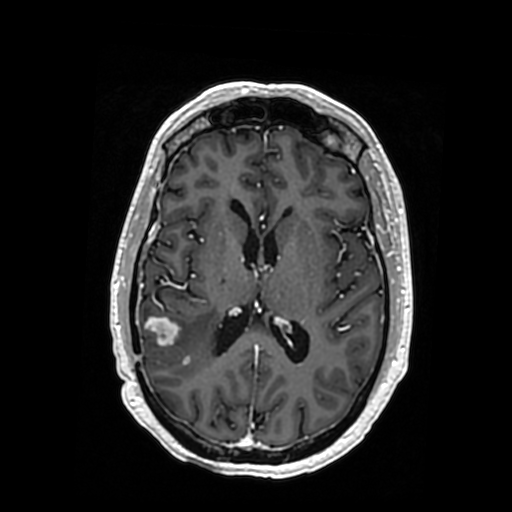
Brain MRI from a brain-tumour surgery series, one axial slice. Slice 169 of 364 in the series (ordered by position). T1-weighted post-contrast. 0.5 mm slice thickness. 512 × 512 image matrix, field of view 260 × 260 mm. From the clinical record (not read from this slice): histopathology: Oligodendroglioma; WHO grade: 3; IDH mutation: yes.
Structures marked on this image (outlined manually by an expert reader):
- tumour: bounding box <146,317,217,363> (left, top, right, bottom; pixels)